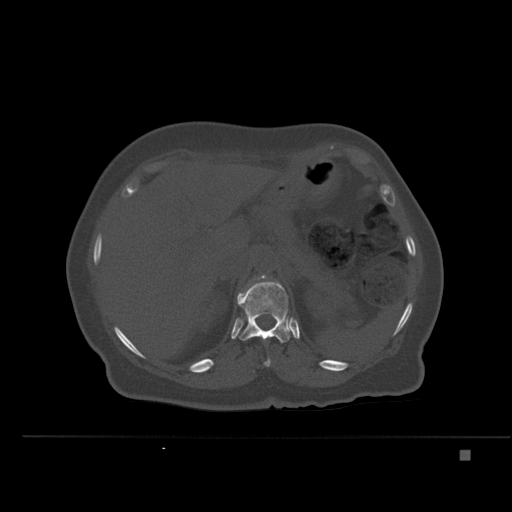
CT including the spine, one axial slice. Slice 254 of 477 in the series (ordered by position). Bone window (W 1800 / L 400 HU). 1.5 mm slice thickness. 512 × 512 image matrix, field of view 422 × 422 mm. Patient: female, 74 years. Case-level facts recorded for this patient, not image findings: primary cancer: colon.
Annotated regions visible in this slice (semi-automatically segmented with operator editing):
- L1 vertebra: bounding box [x1, y1, x2, y2] px = [248, 275, 267, 286]
- T11 vertebra: [264, 358, 271, 366]
- T12 vertebra: [237, 281, 292, 343]